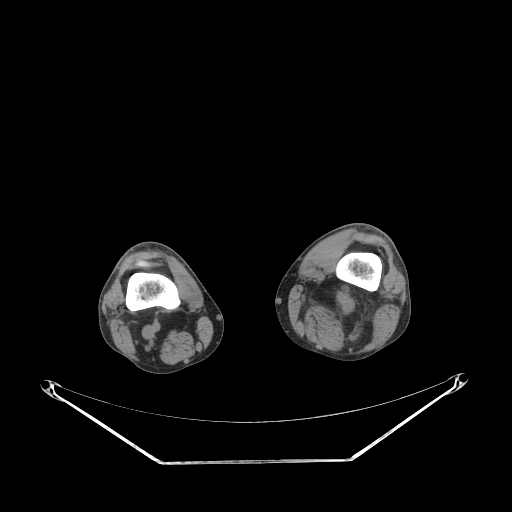
CT of an extremity soft-tissue mass (from a PET/CT study), one axial slice. Reconstruction kernel STANDARD. 140 kVp. Soft-tissue window (W 400 / L 40 HU). 3.75 mm slice thickness. 512 × 512 image matrix, field of view 500 × 500 mm. Male patient. Case-level facts recorded for this patient, not image findings: histological type: undifferentiated pleomorphic liposarcoma; grade: high; site of the primary tumour: left thigh.
Annotated regions visible in this slice (expert contour drawn on MRI and transferred to this co-registered scan by the dataset authors):
- gross tumour volume including surrounding oedema: box from (x=297, y=286) to (x=375, y=323) px